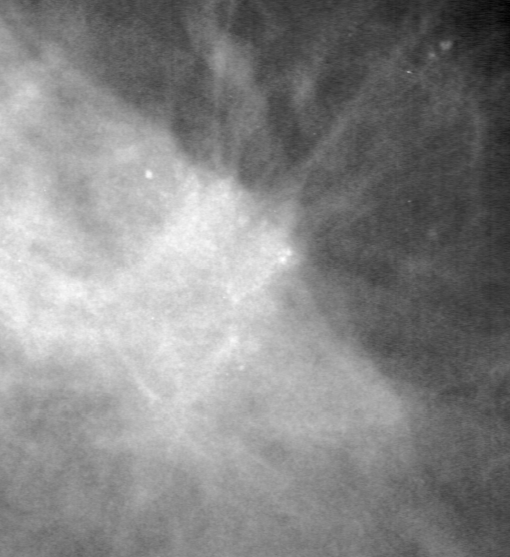
Cropped region of a digitized screen-film mammogram centred on a radiologist-marked abnormality; right breast; CC view; BI-RADS breast density category 4 (scale 1–4).
- Marked abnormality: calcifications, morphology pleomorphic, distribution clustered; BI-RADS assessment category 4; pathology (as recorded): malignant.